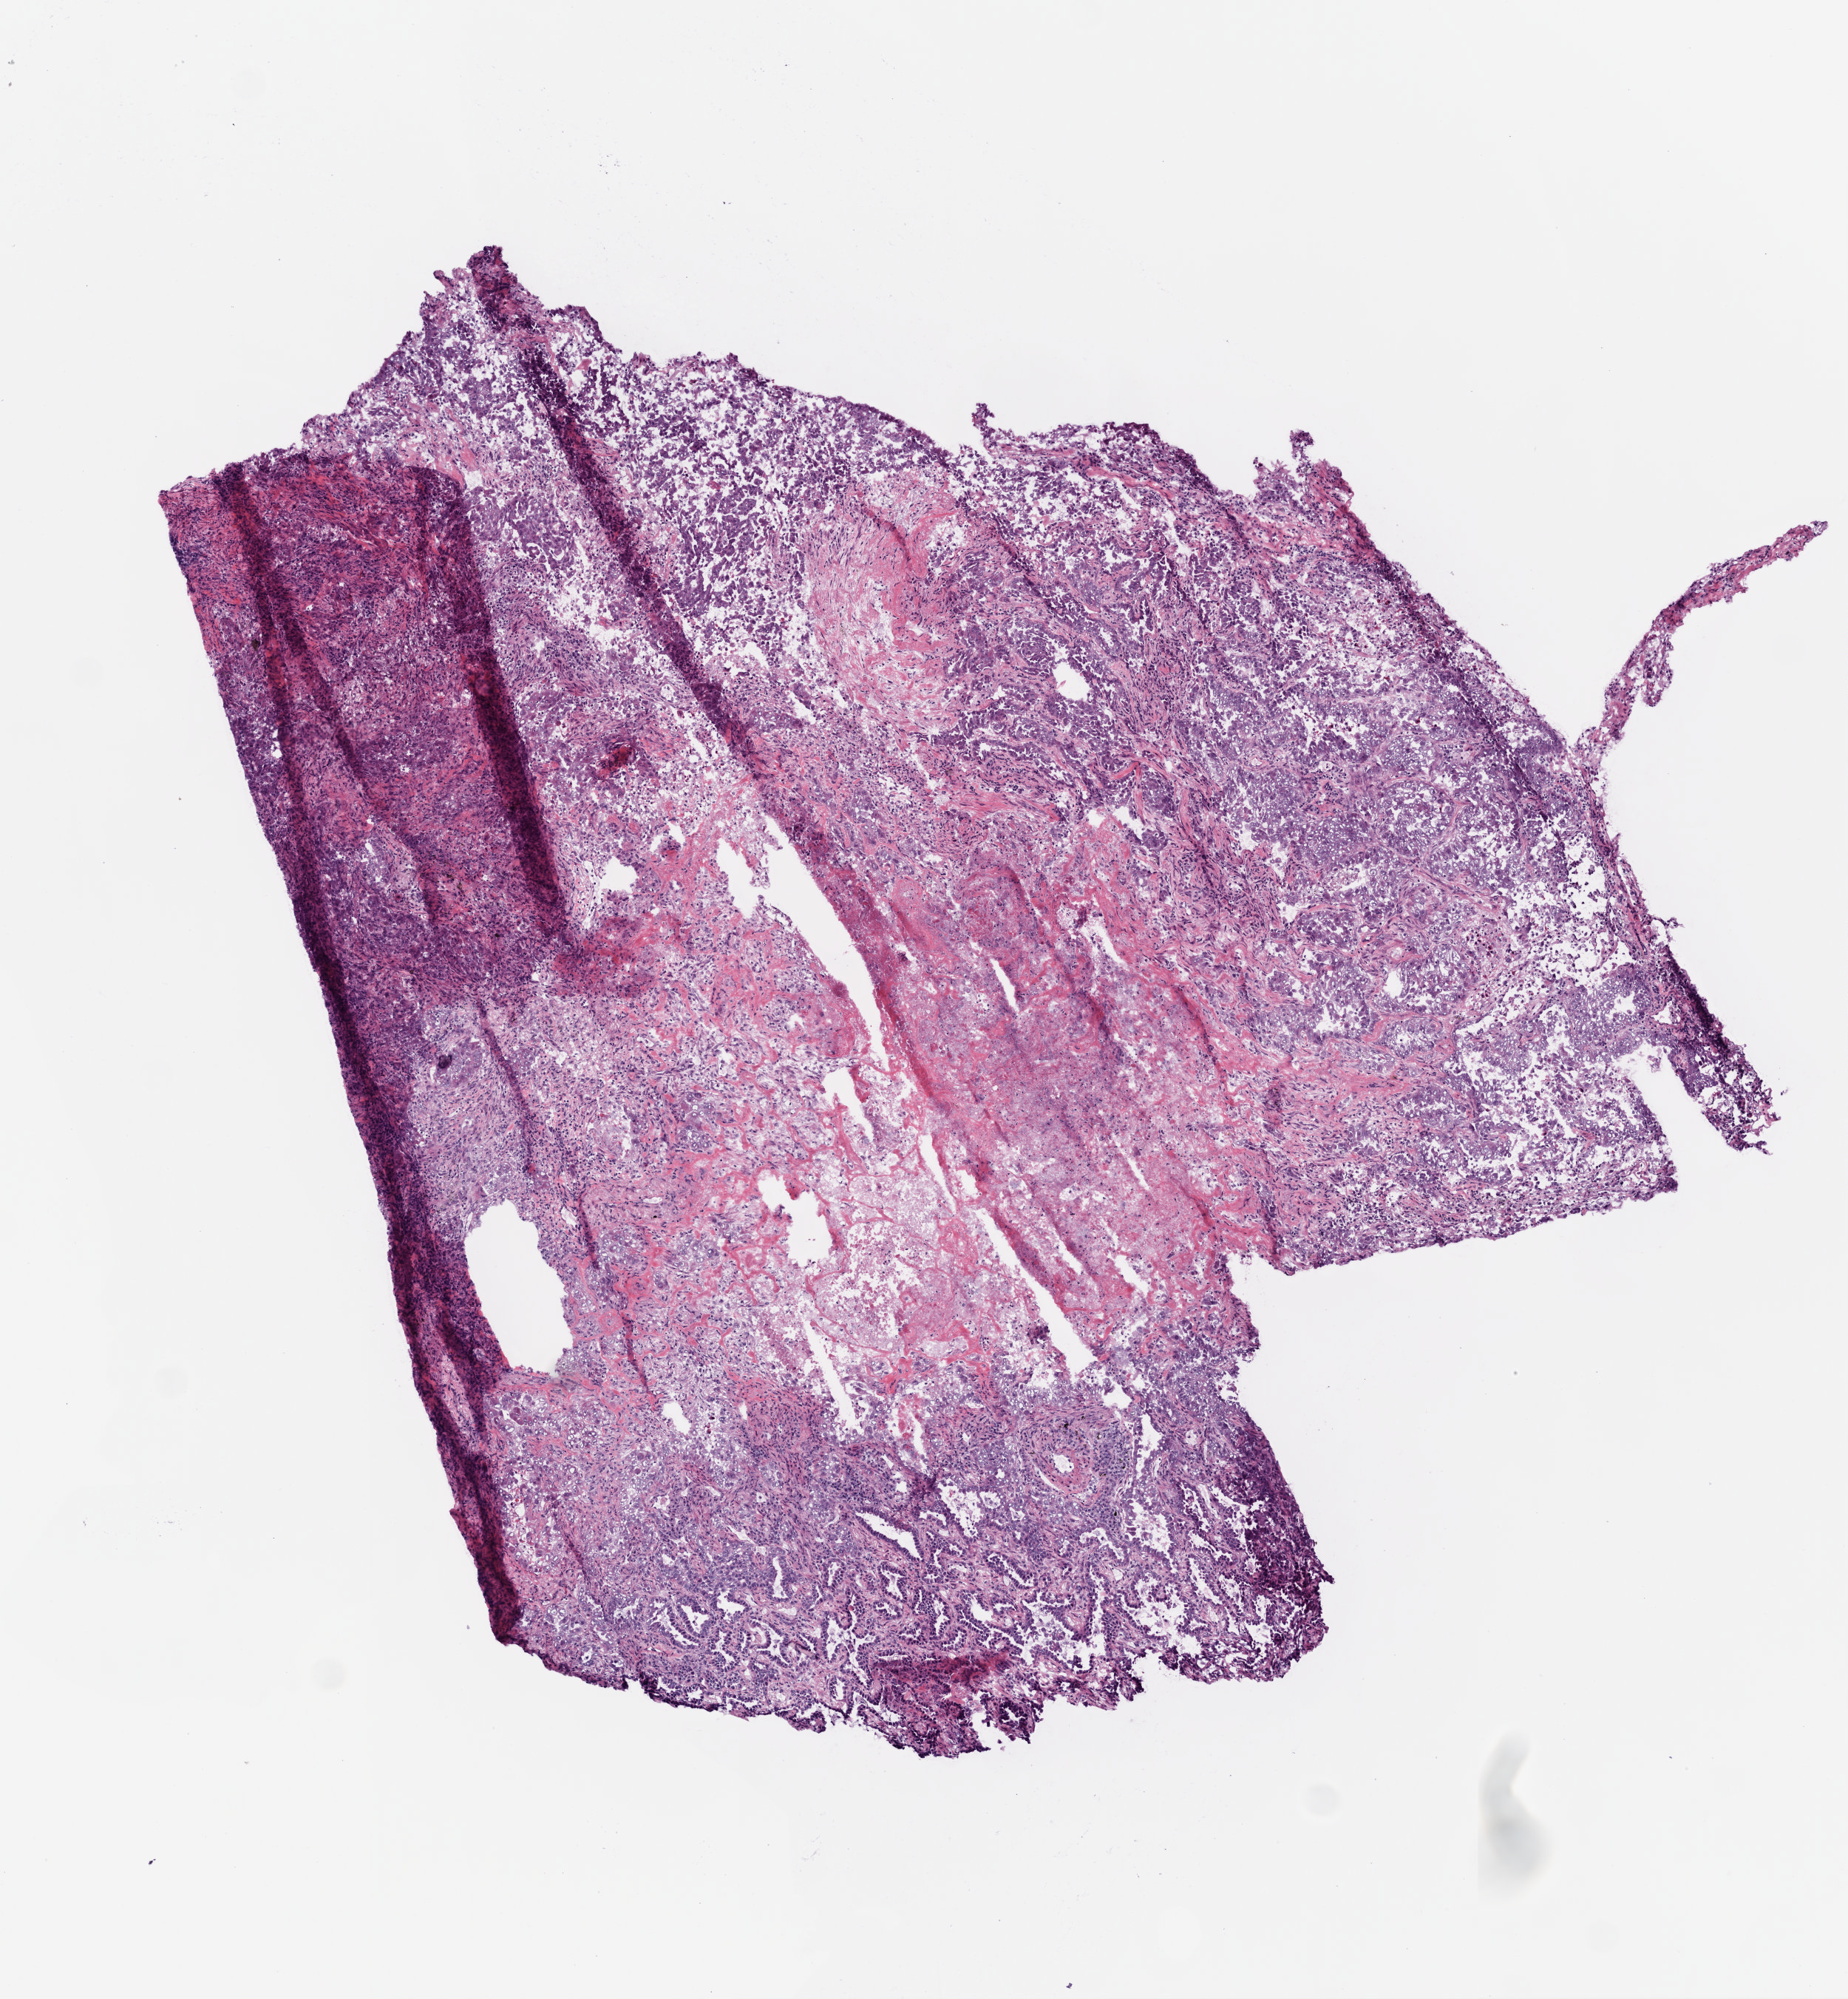
Whole-slide histology image, Hematoxylin and eosin (H&E) stained, whole scanned area (about 5.0 x 5.4 mm, acquisition: 20x scan) shown as a low-resolution overview. Frozen section. Lung, primary tumour sample. Female, age 57 years at initial diagnosis. Slide review estimates, as recorded: tumour cells 70%, tumour nuclei 70%, normal cells 0%, stromal cells 10%, necrosis 20%.
* AJCC pathologic stage: IIB
* pathologic diagnosis: Adenocarcinoma, NOS (lower lobe, lung)
* laterality: right